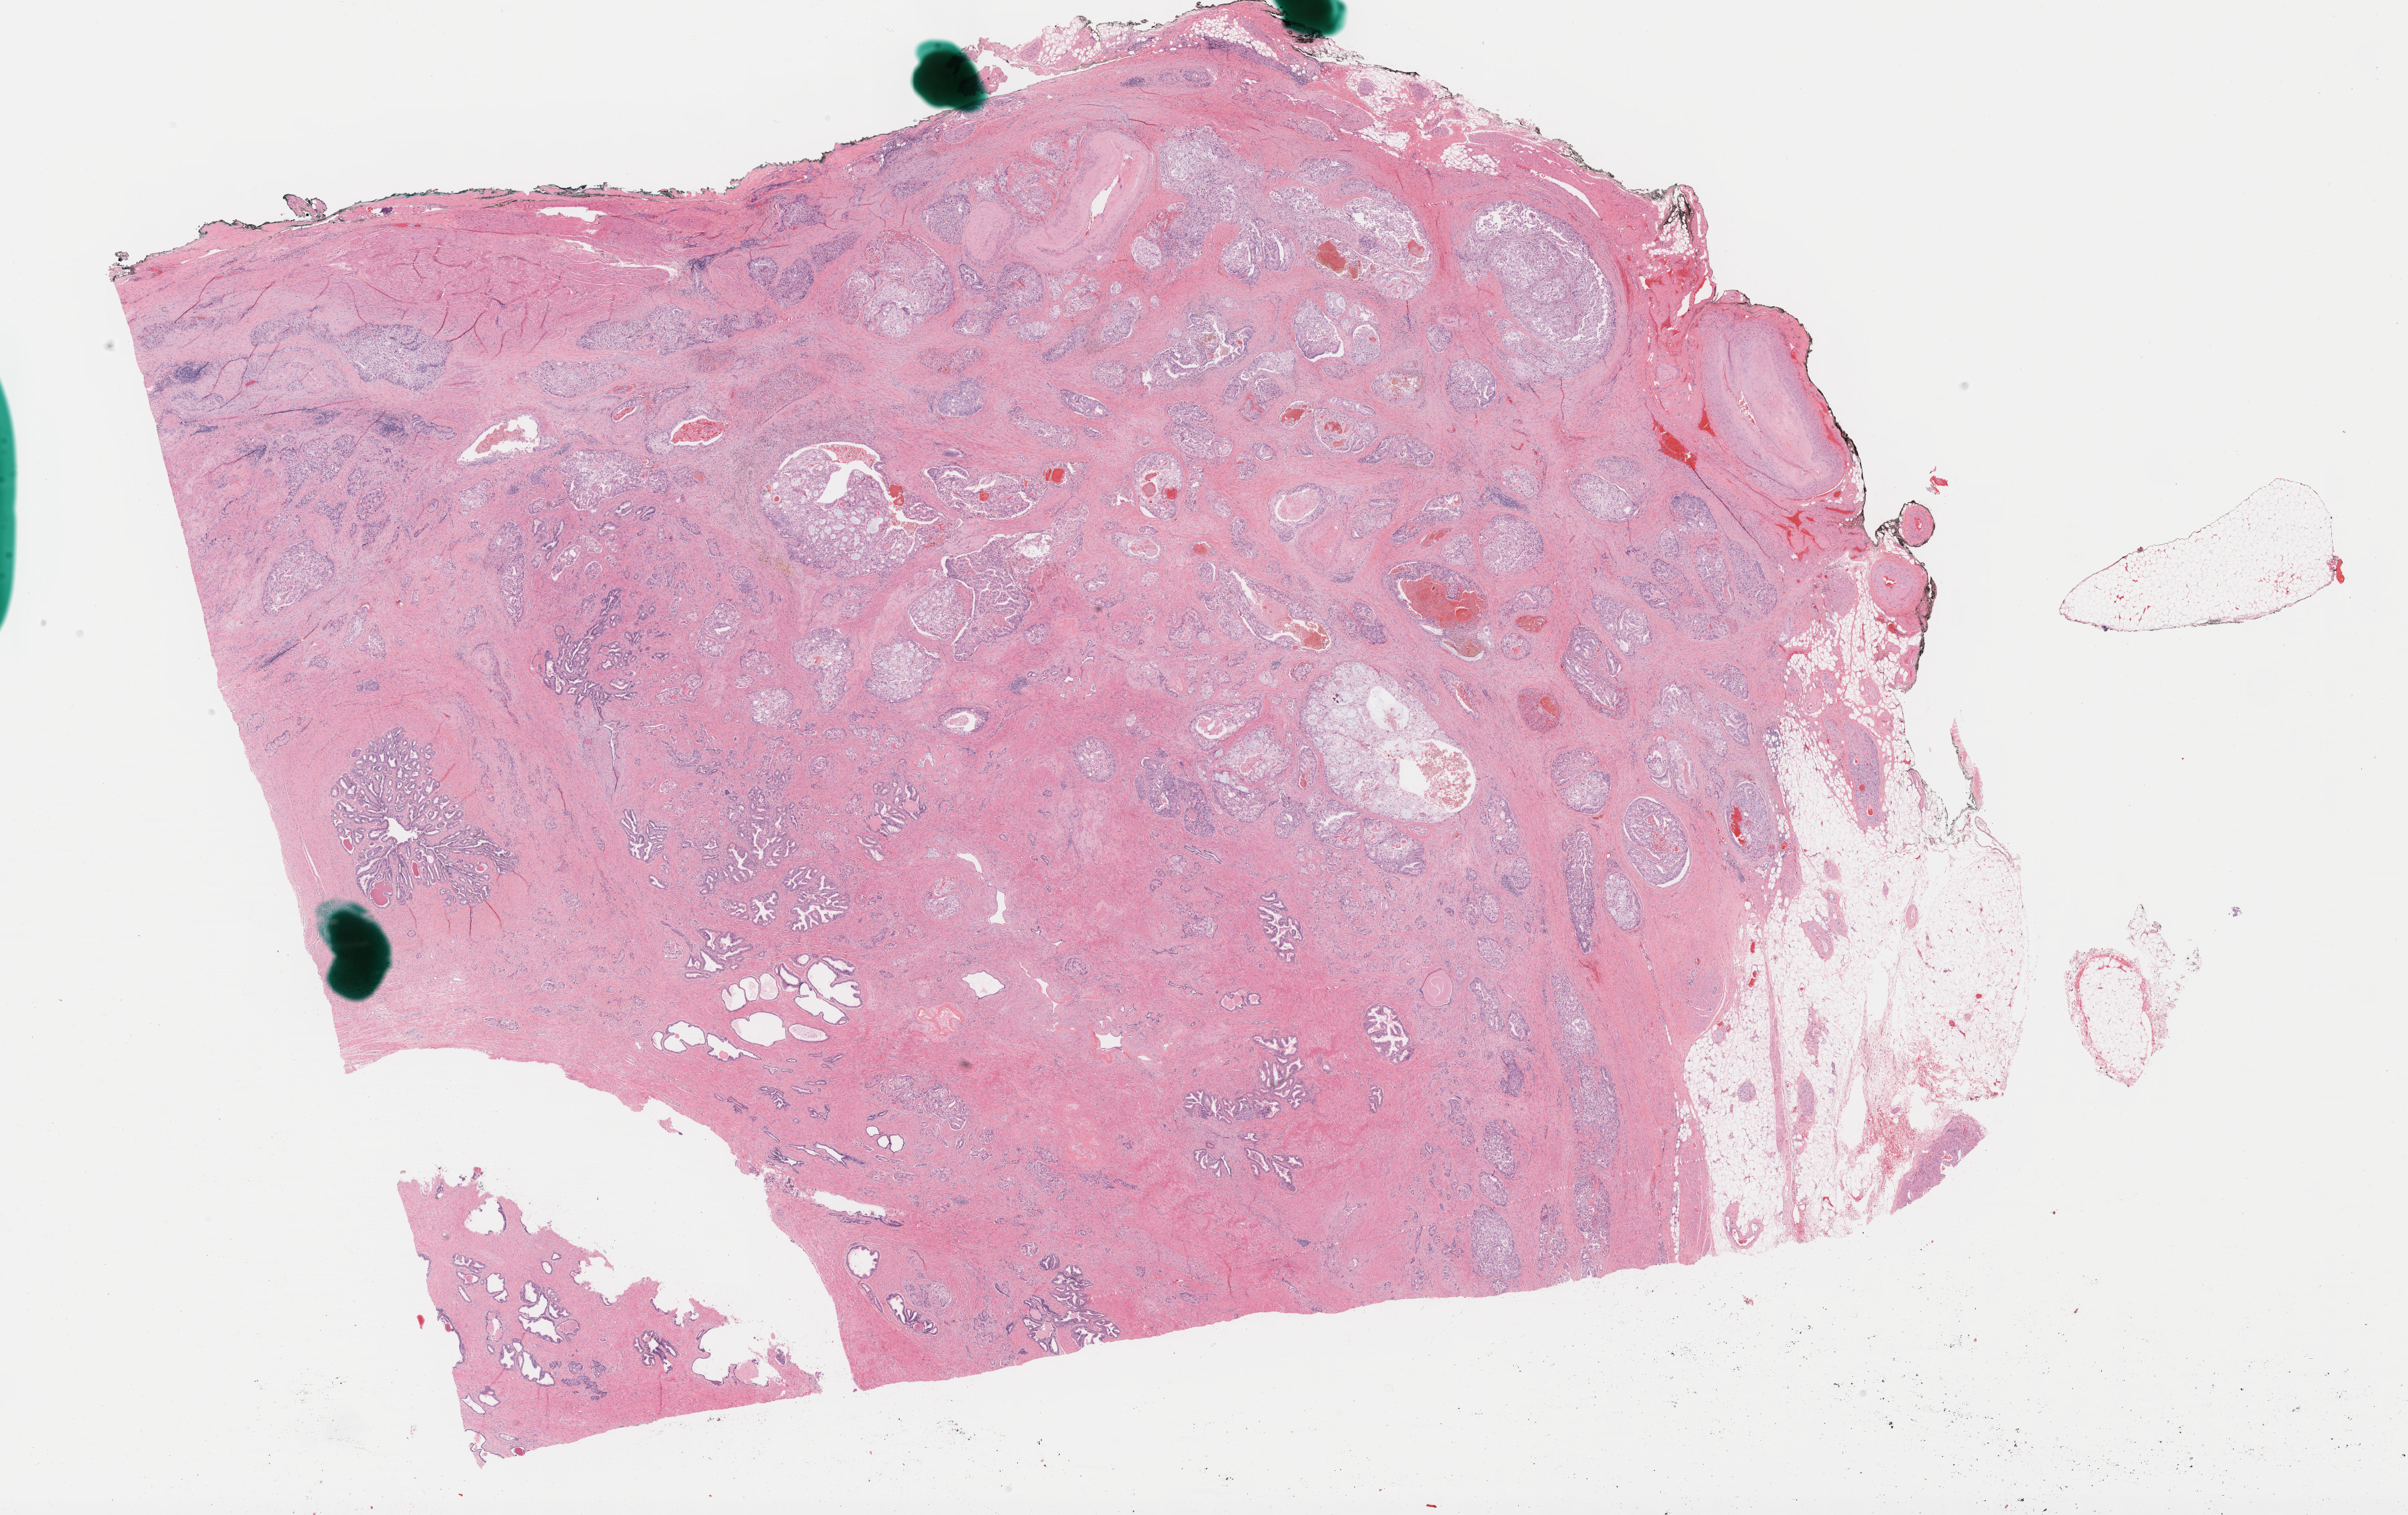
Whole-slide histology image, H&E, whole scanned area (about 29.2 x 18.4 mm) shown as a low-resolution overview, formalin-fixed paraffin-embedded (FFPE) diagnostic section, primary tumour sample from the prostate. Patient: male, age at initial diagnosis 59 years. Gleason score: 9 (4+5).
Laterality: bilateral. Histologic diagnosis: Adenocarcinoma, NOS (prostate gland). Lymph nodes positive (case pathology): 1 of 20 examined.